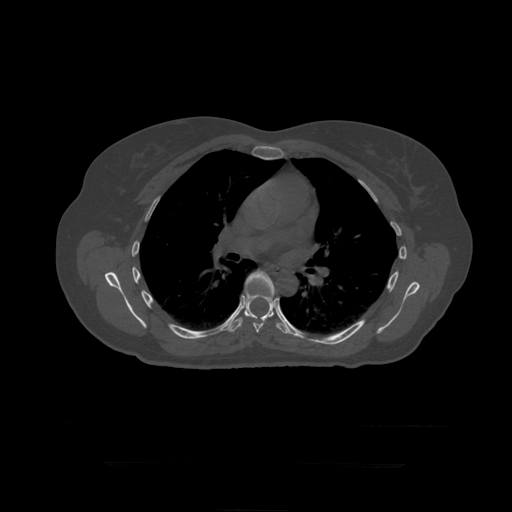
CT including the spine, one axial slice. 120 kVp. Bone window (W 1800 / L 400 HU). 1.25 mm slice thickness. 512 × 512 image matrix, field of view 450 × 450 mm. Patient age 41 years. From the clinical record (not read from this slice): primary cancer: breast.
Structures marked on this image (semi-automatic segmentation, software-assisted and operator-edited):
- T7 vertebra: bounding box <242,270,276,333> (left, top, right, bottom; pixels)
- T8 vertebra: <229,286,289,334>